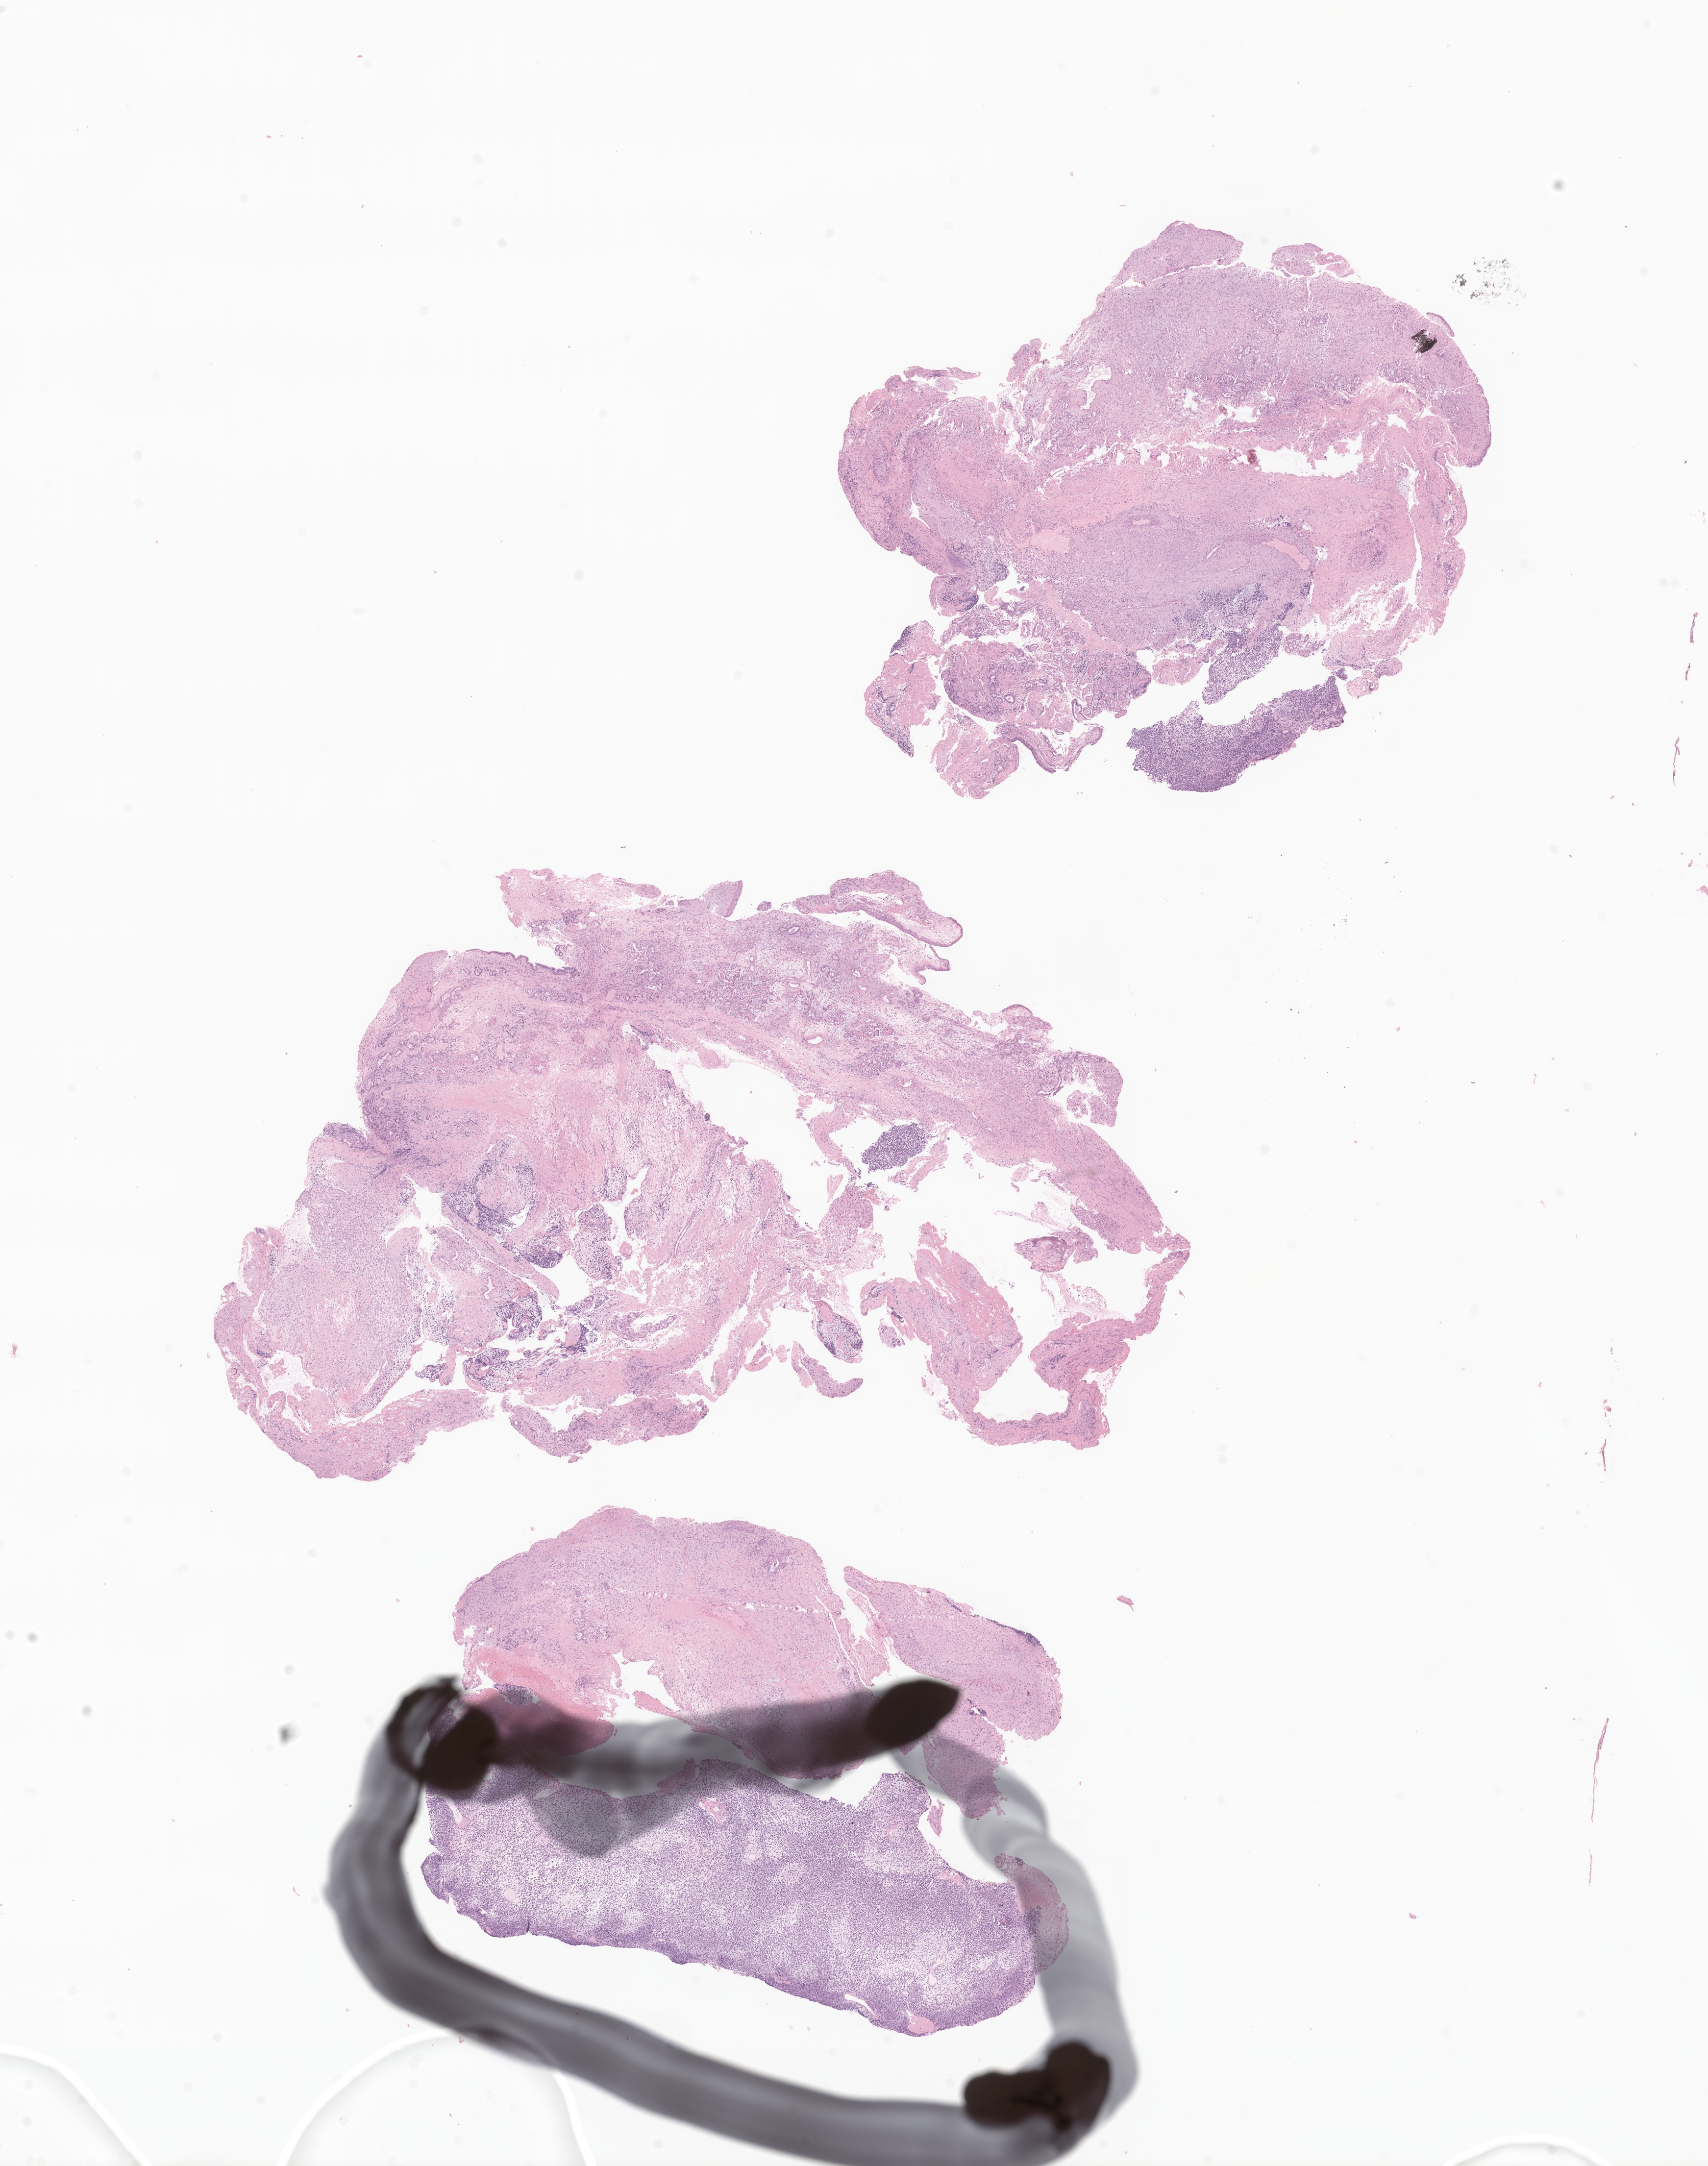
H&E whole-slide image of tumor tissue from the nasopharynx — a low-resolution overview of the entire scanned area, about 14.7 x 18.6 mm, formalin-fixed, paraffin-embedded (FFPE) tissue. Female patient, age 52 months (4 years 4 months).
Diagnosis (ICD-O-3 morphology term): Embryonal rhabdomyosarcoma, NOS.